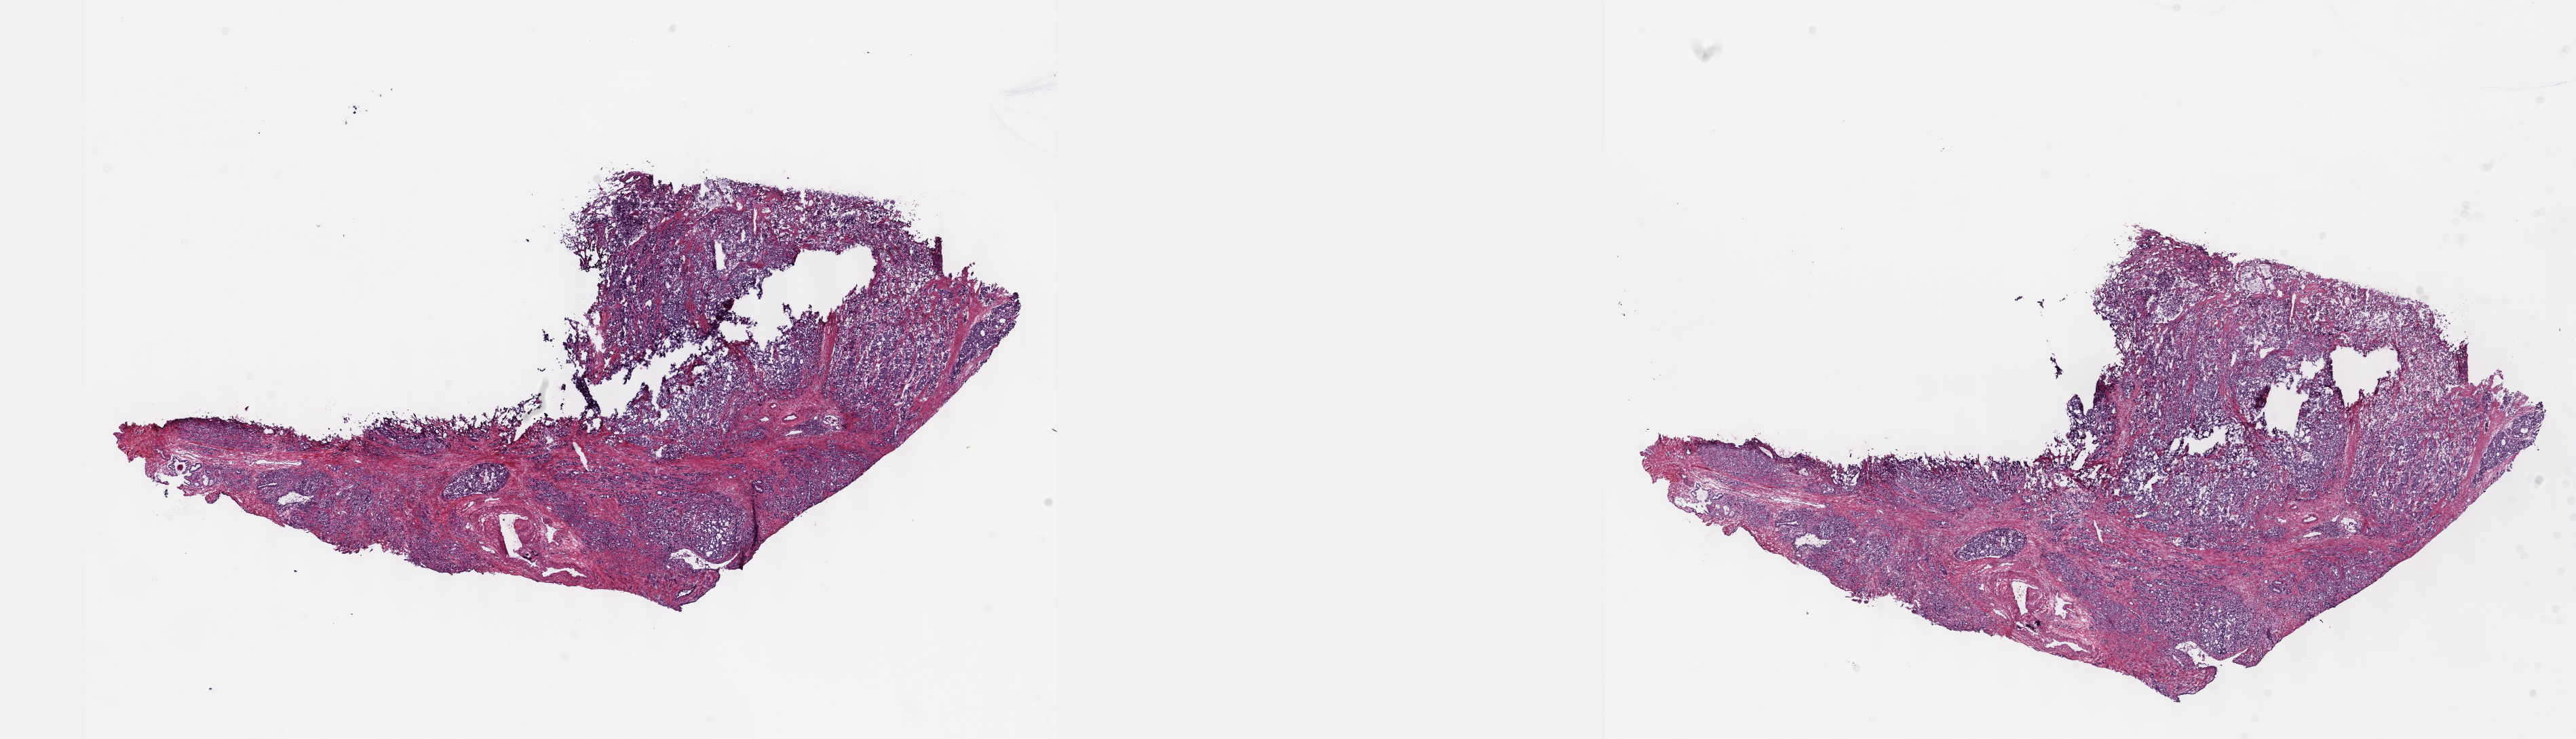
H&E whole-slide image — a low-resolution overview of the entire scanned area, about 30.7 x 8.8 mm (slide scanned at 40x), frozen section, prostate, primary tumour sample. Patient: male, age at initial diagnosis 68 years. Gleason score: 9 (4+5). Composition of this section per pathologist review: tumour cells 70%, tumour nuclei 80%, normal cells 0%, stromal cells 30%, necrosis 0%. Inflammatory infiltration, as recorded: lymphocyte infiltration 0%, monocyte infiltration 0%, neutrophil infiltration 0%.
Pathologic diagnosis: Adenocarcinoma, NOS (prostate gland). Laterality: bilateral.